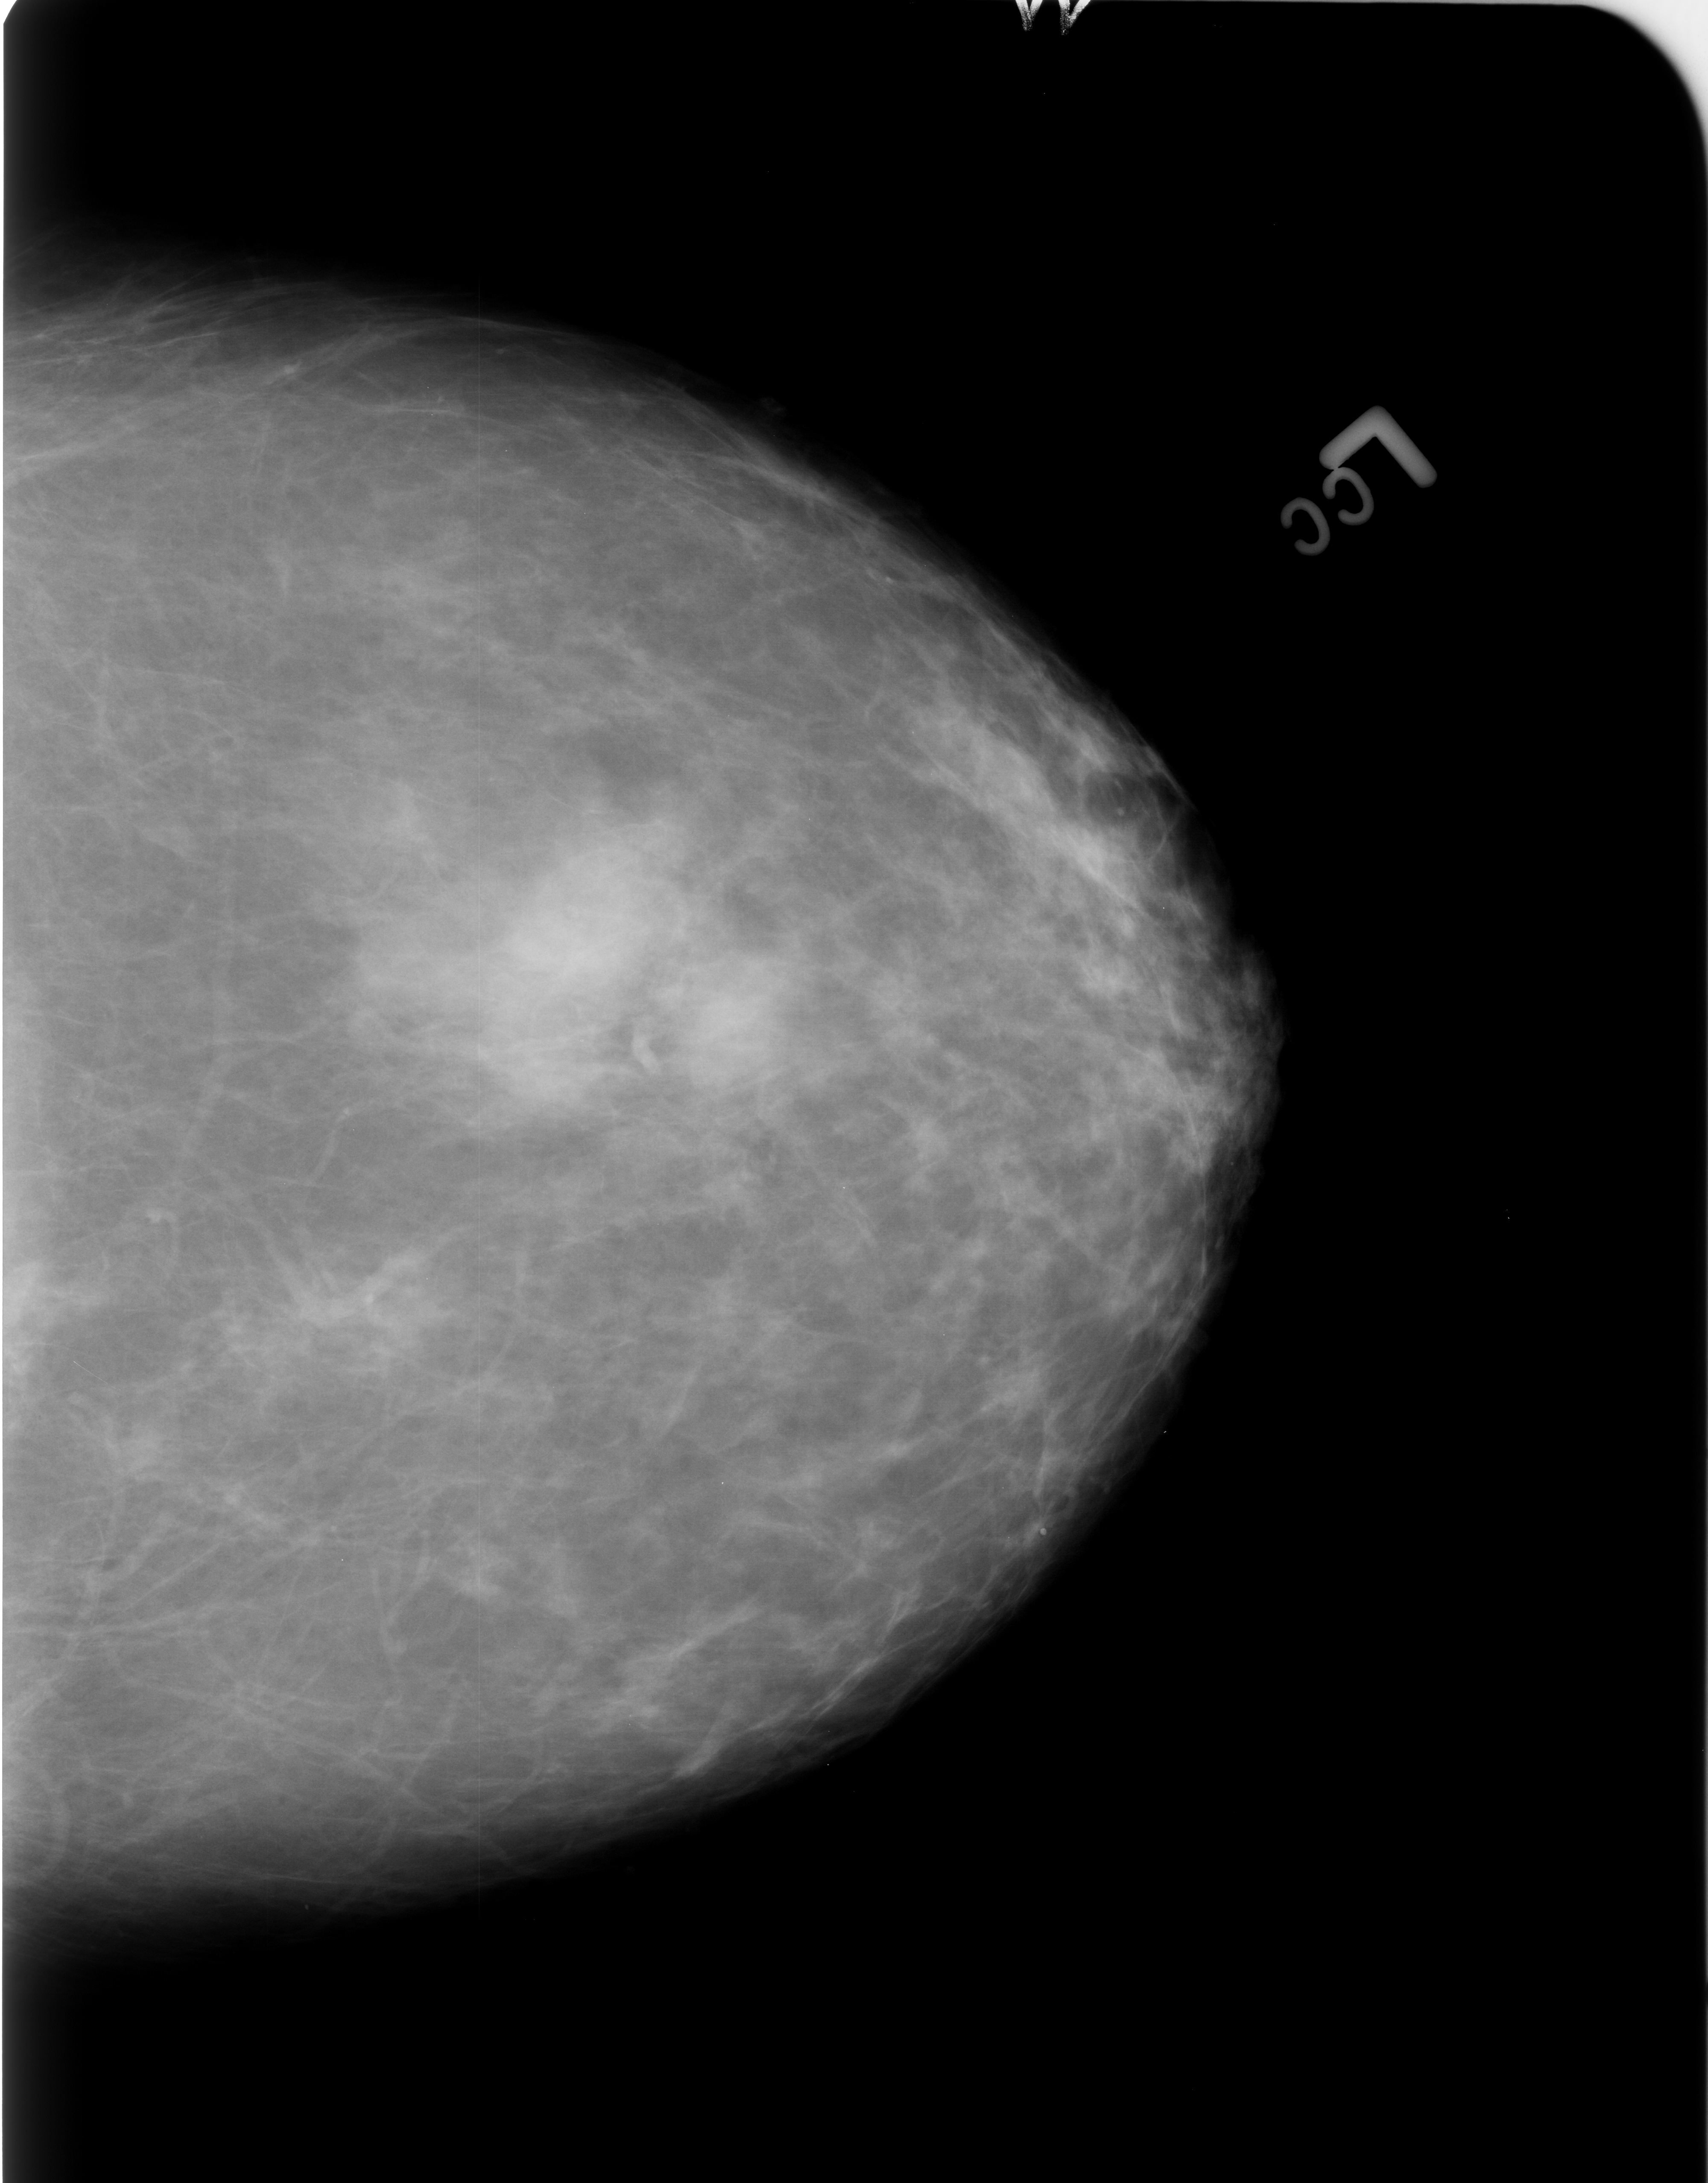
Mammogram (digitized film); left breast; craniocaudal (CC) view; BI-RADS breast density category 2 (scale 1–4).
Abnormality record for this image: calcifications, morphology round and regular; BI-RADS assessment category 2; subtlety rating 4 on a 1 (subtle) to 5 (obvious) scale; benign without callback (not worked up further).